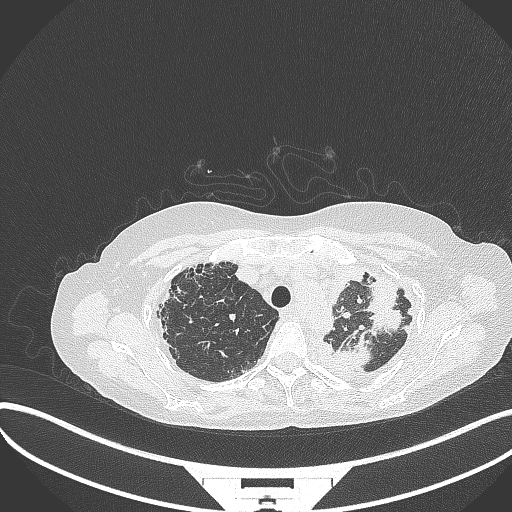
Chest CT, one axial slice; position 273 of 373 along the scan axis; reconstruction kernel B70f; lung window (W 1500 / L -600 HU); 512 × 512 image matrix. Female patient, age 56 years. Case-level facts recorded for this patient, not image findings: clinical TNM (as recorded): T1 N0 M0.
Structures marked on this image (rectangle marked by the reading radiologist):
- lung tumour (recorded histology: adenocarcinoma): bounding box <336,336,370,369> (left, top, right, bottom; pixels)
- lung tumour (recorded histology: adenocarcinoma): <361,270,405,335>